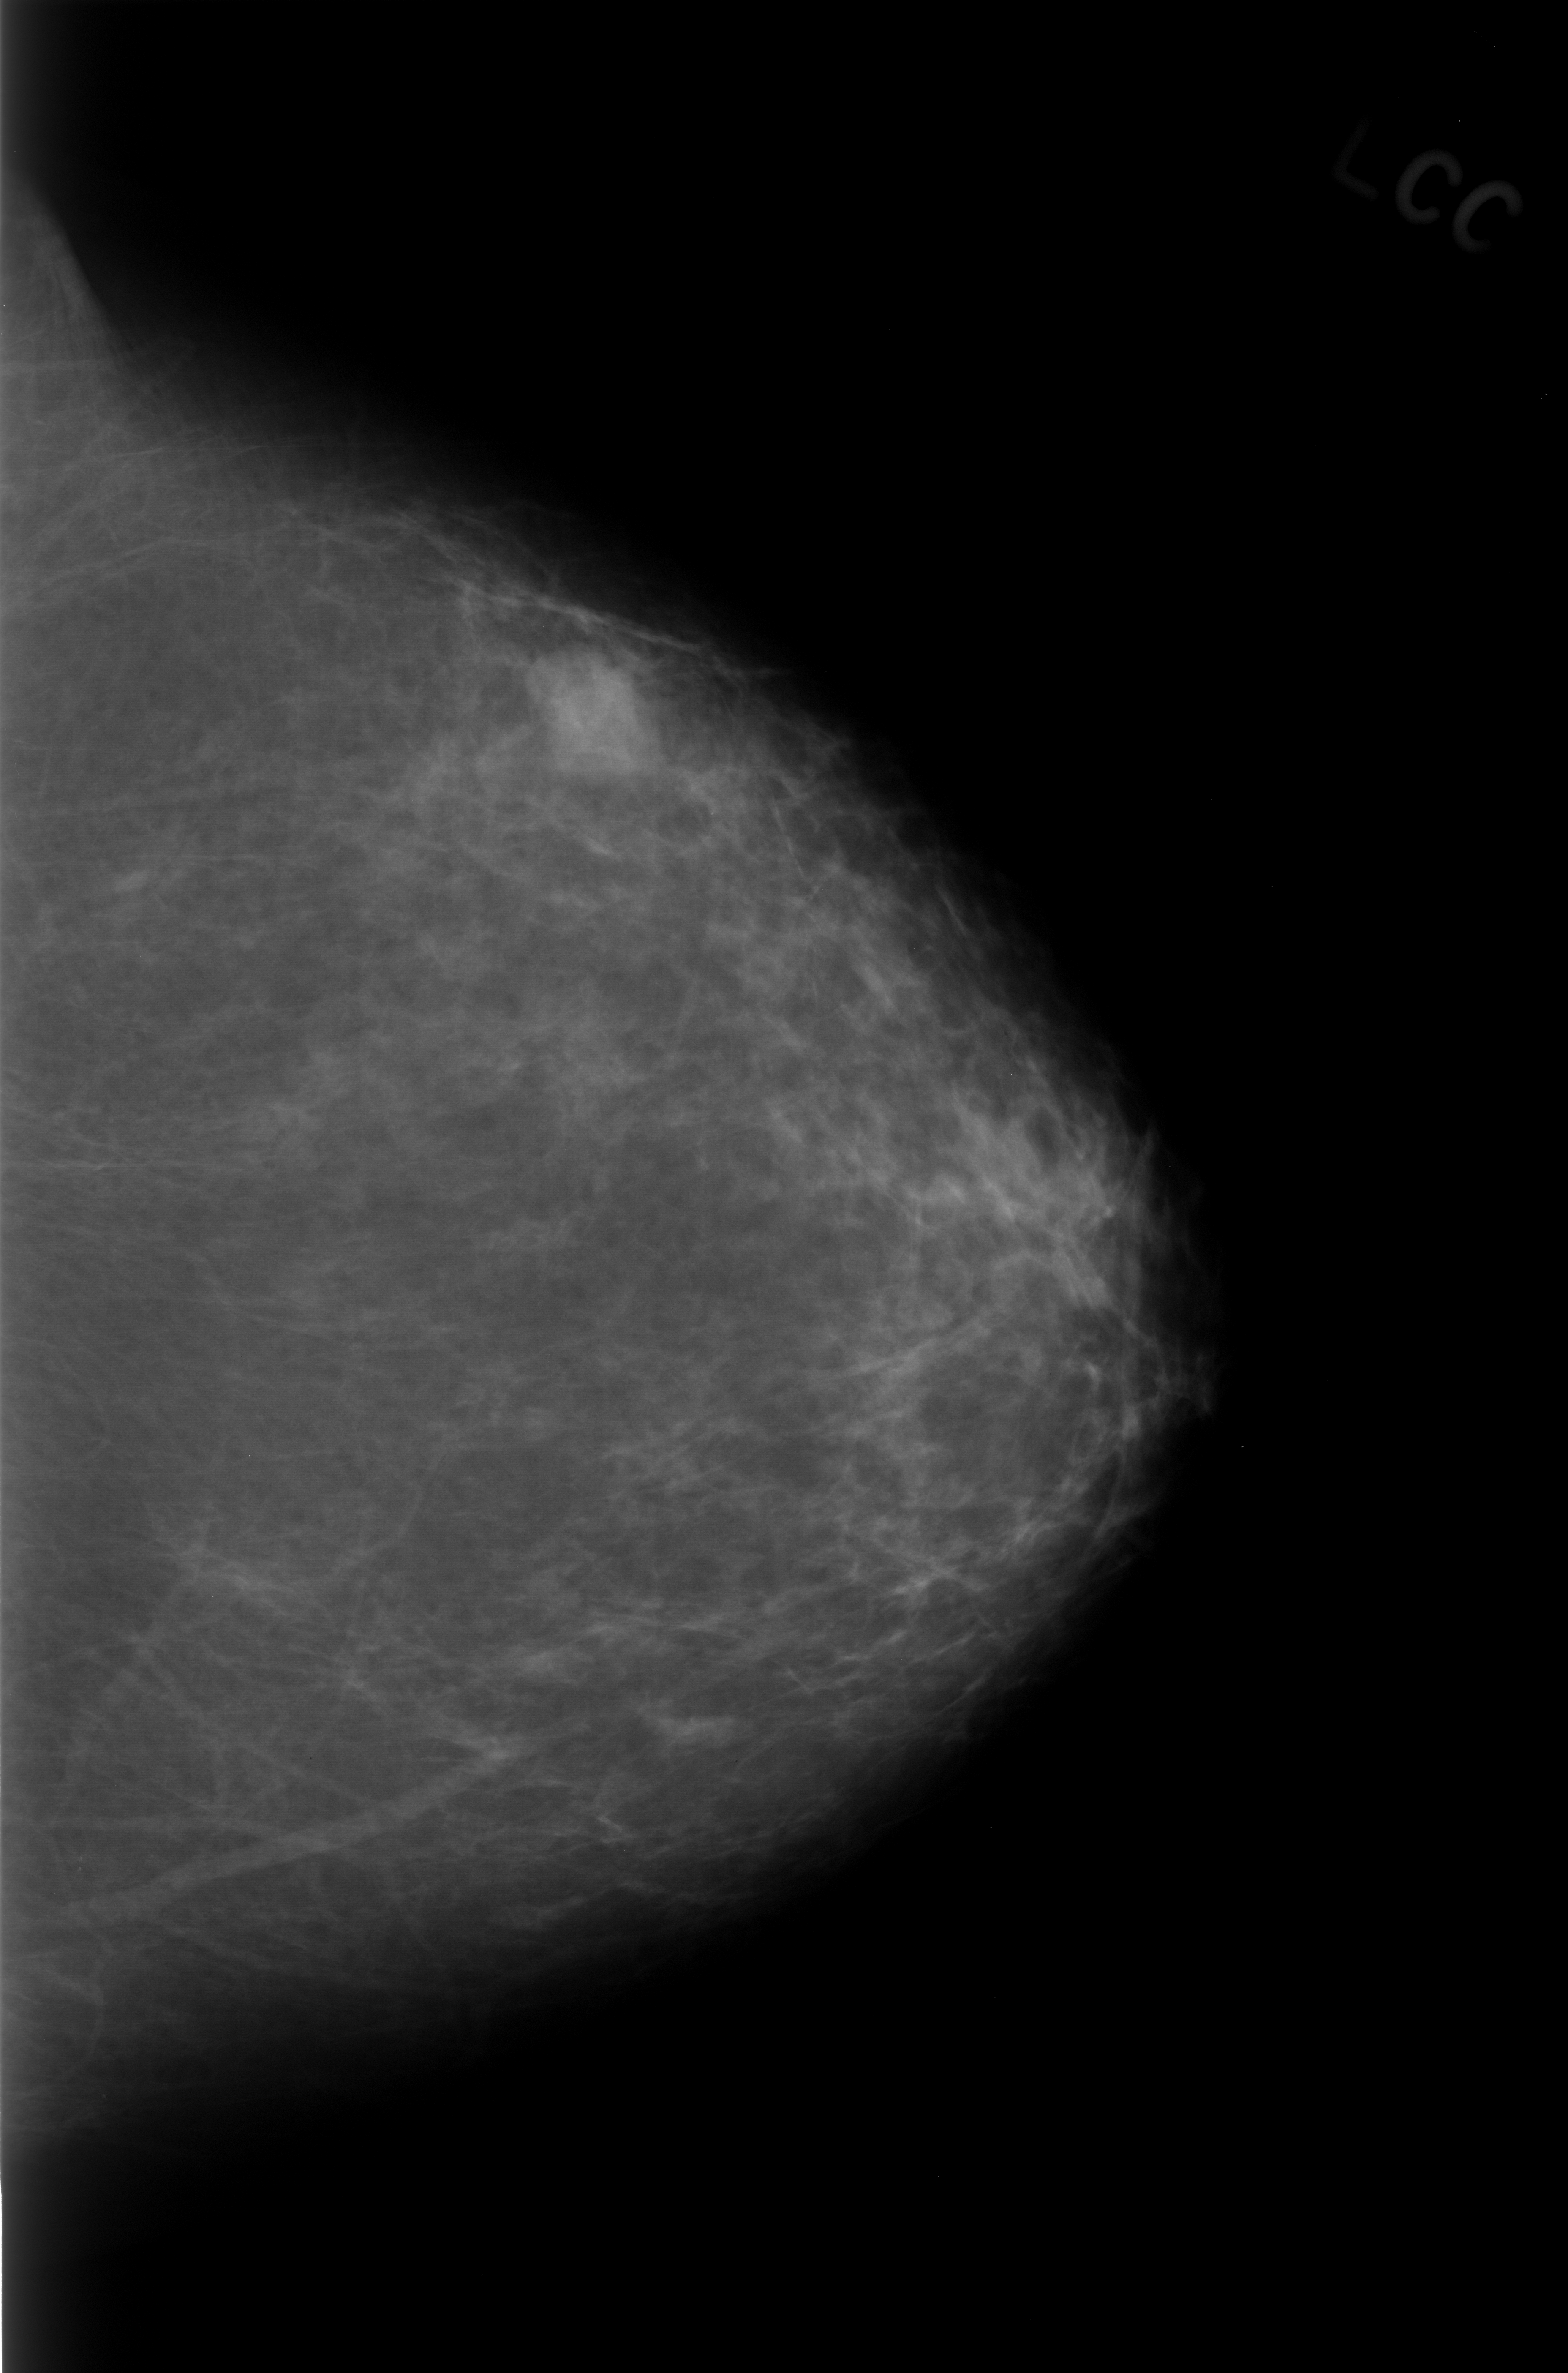
Scanned film-screen mammogram; left breast; craniocaudal (CC) view.
Abnormality record for this image: mass, shape lobulated, margins obscured; BI-RADS assessment category 3; pathology result (as recorded, not read from the image): benign.